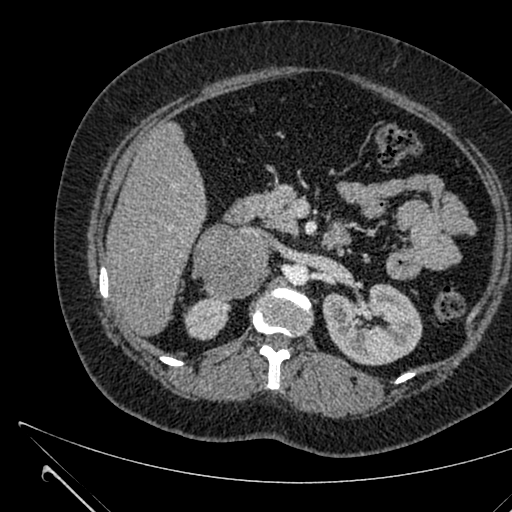
Contrast-enhanced abdominal CT, one axial slice. Slice 379 of 731 in the series (ordered by position). Intravenous contrast given. Soft-tissue window (W 400 / L 40 HU). 1 mm slice thickness. 512 × 512 image matrix, field of view 376 × 376 mm. Female patient, age 36 years. Case-level facts recorded for this patient, not image findings: diagnosis: adrenocortical carcinoma; tumour side: right adrenal; tumour size at pathology: 10 cm; Ki-67 index: 20 %; stage (as recorded): 4.
Structures marked on this image (semi-automatic segmentation, software-assisted and operator-edited):
- mass: bounding box [x1, y1, x2, y2] px = [194, 225, 269, 299]